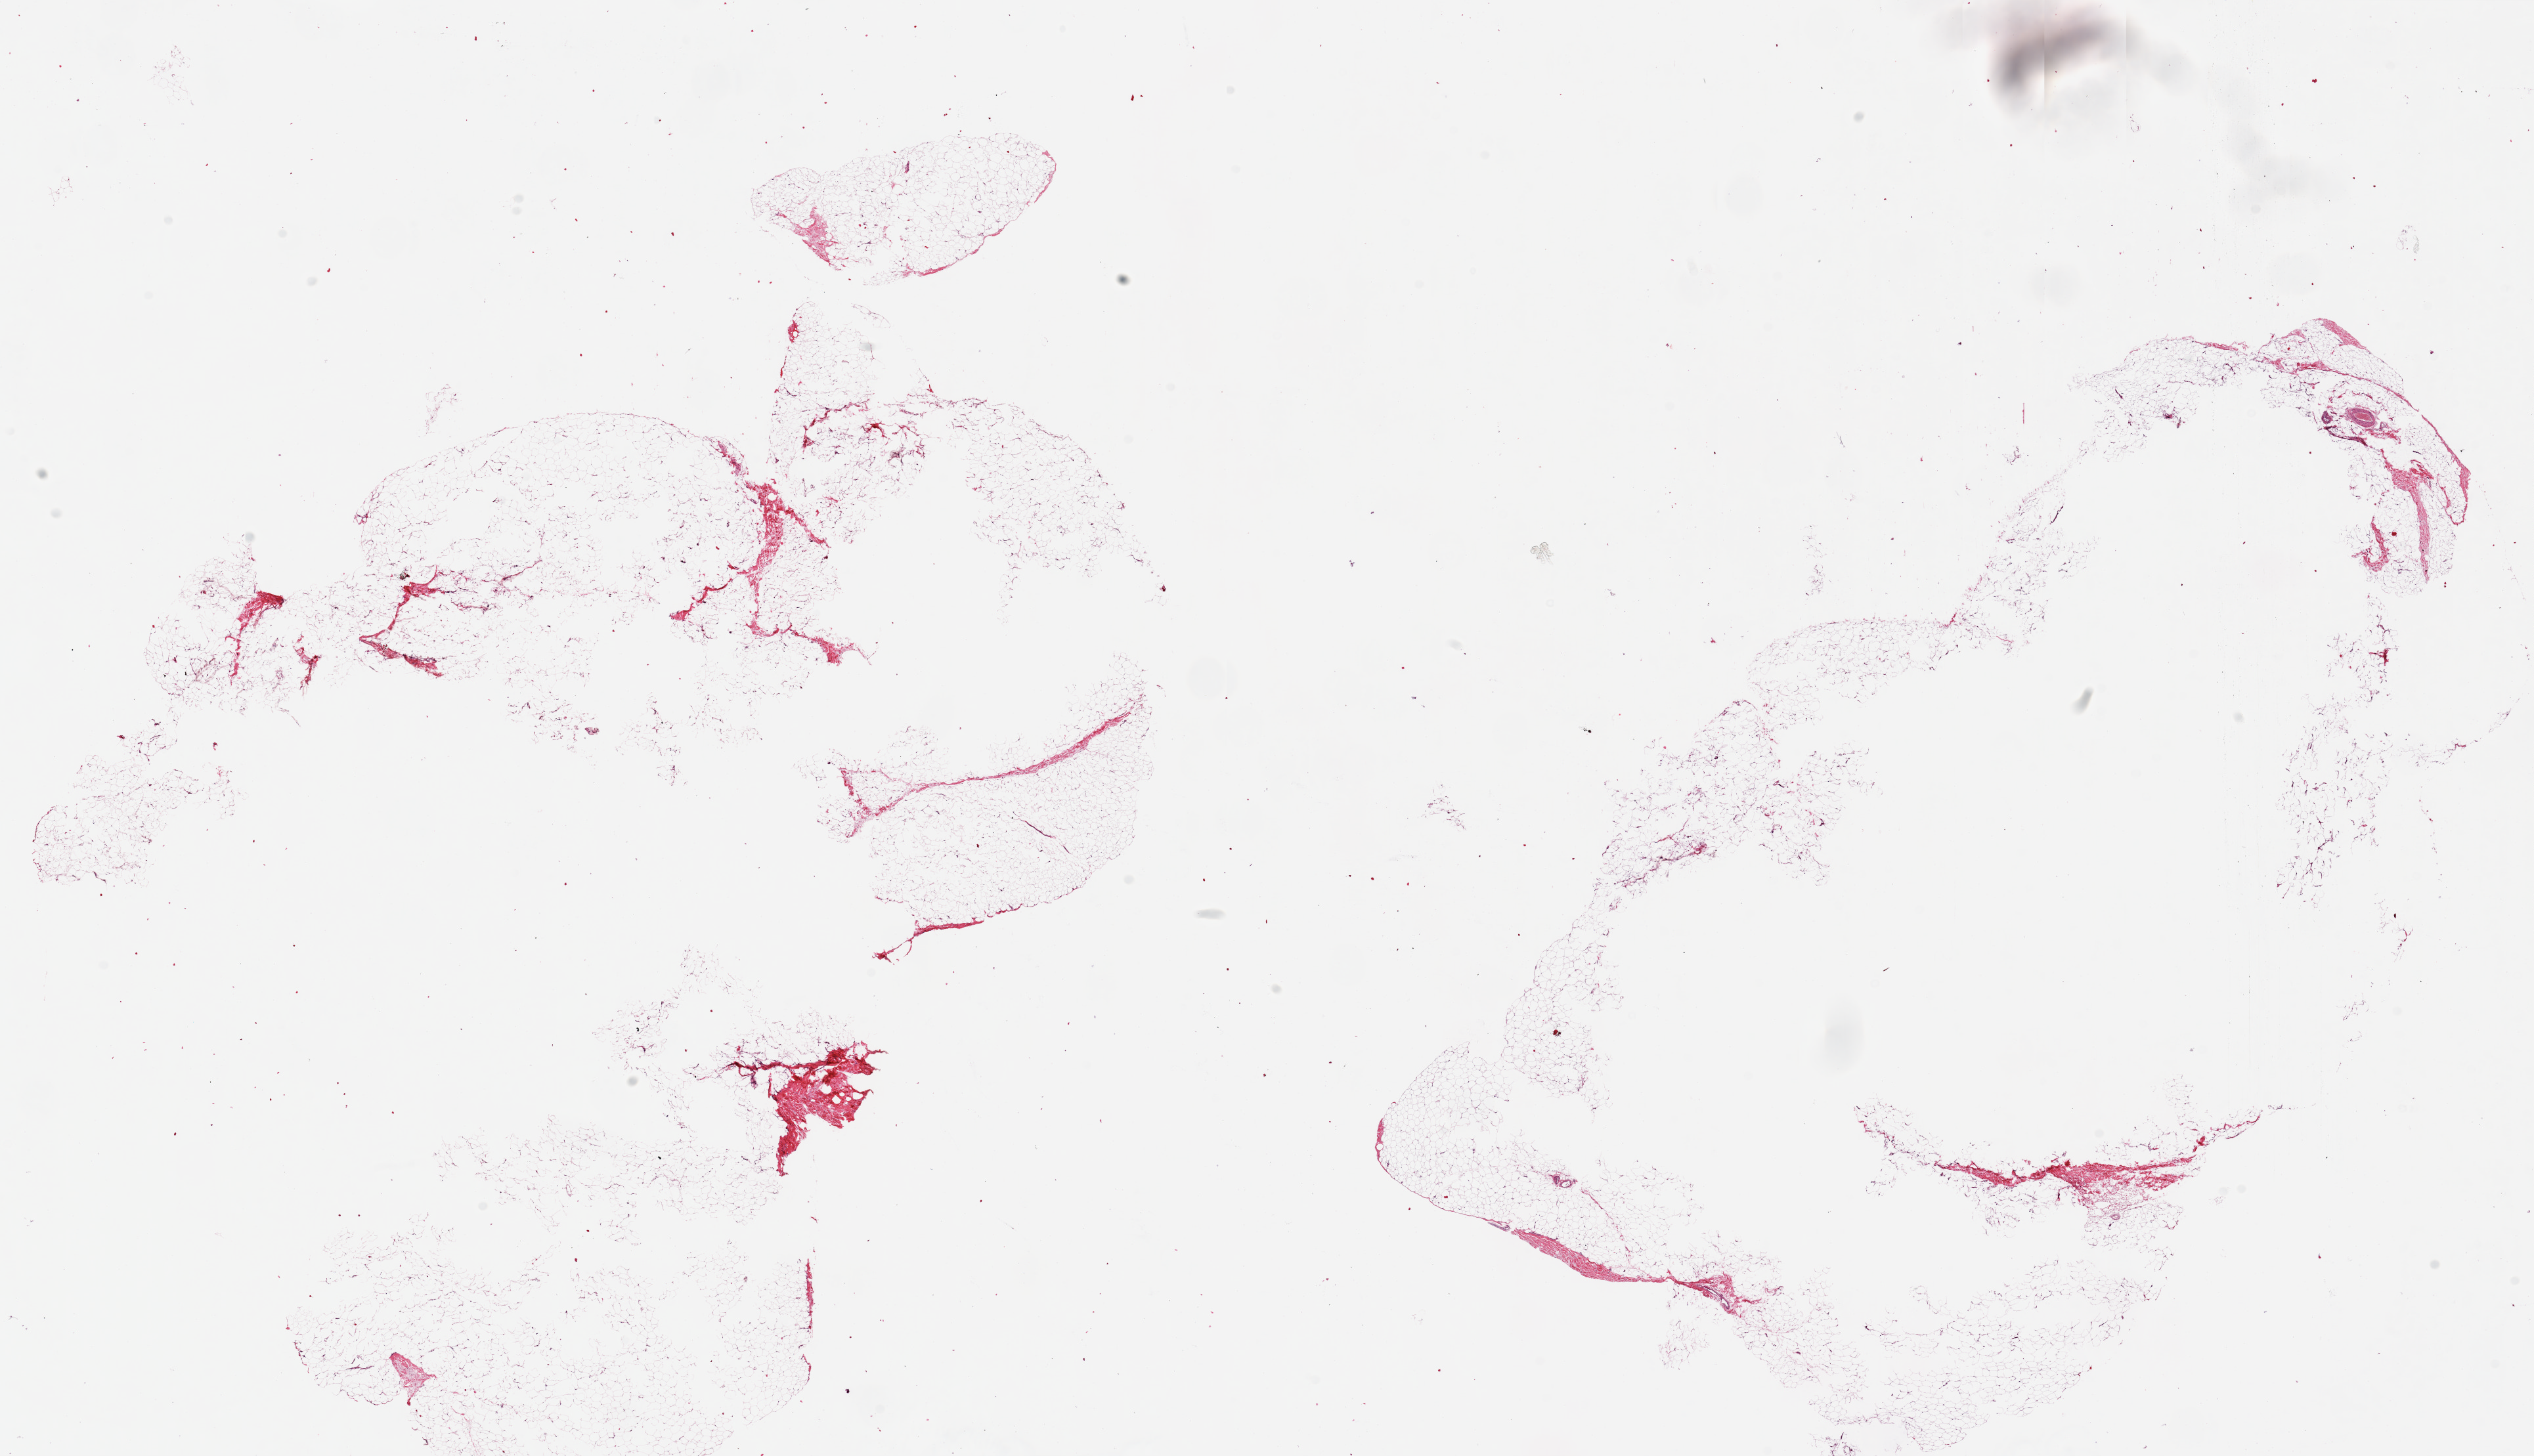
Digitized H&E-stained section, whole scanned area (about 30.5 x 17.5 mm) shown as a low-resolution overview, PAXgene-fixed, paraffin-embedded tissue, target tissue: adipose tissue, donor tissue sample.
Review note (as recorded): 2 pieces ~13x8mm.